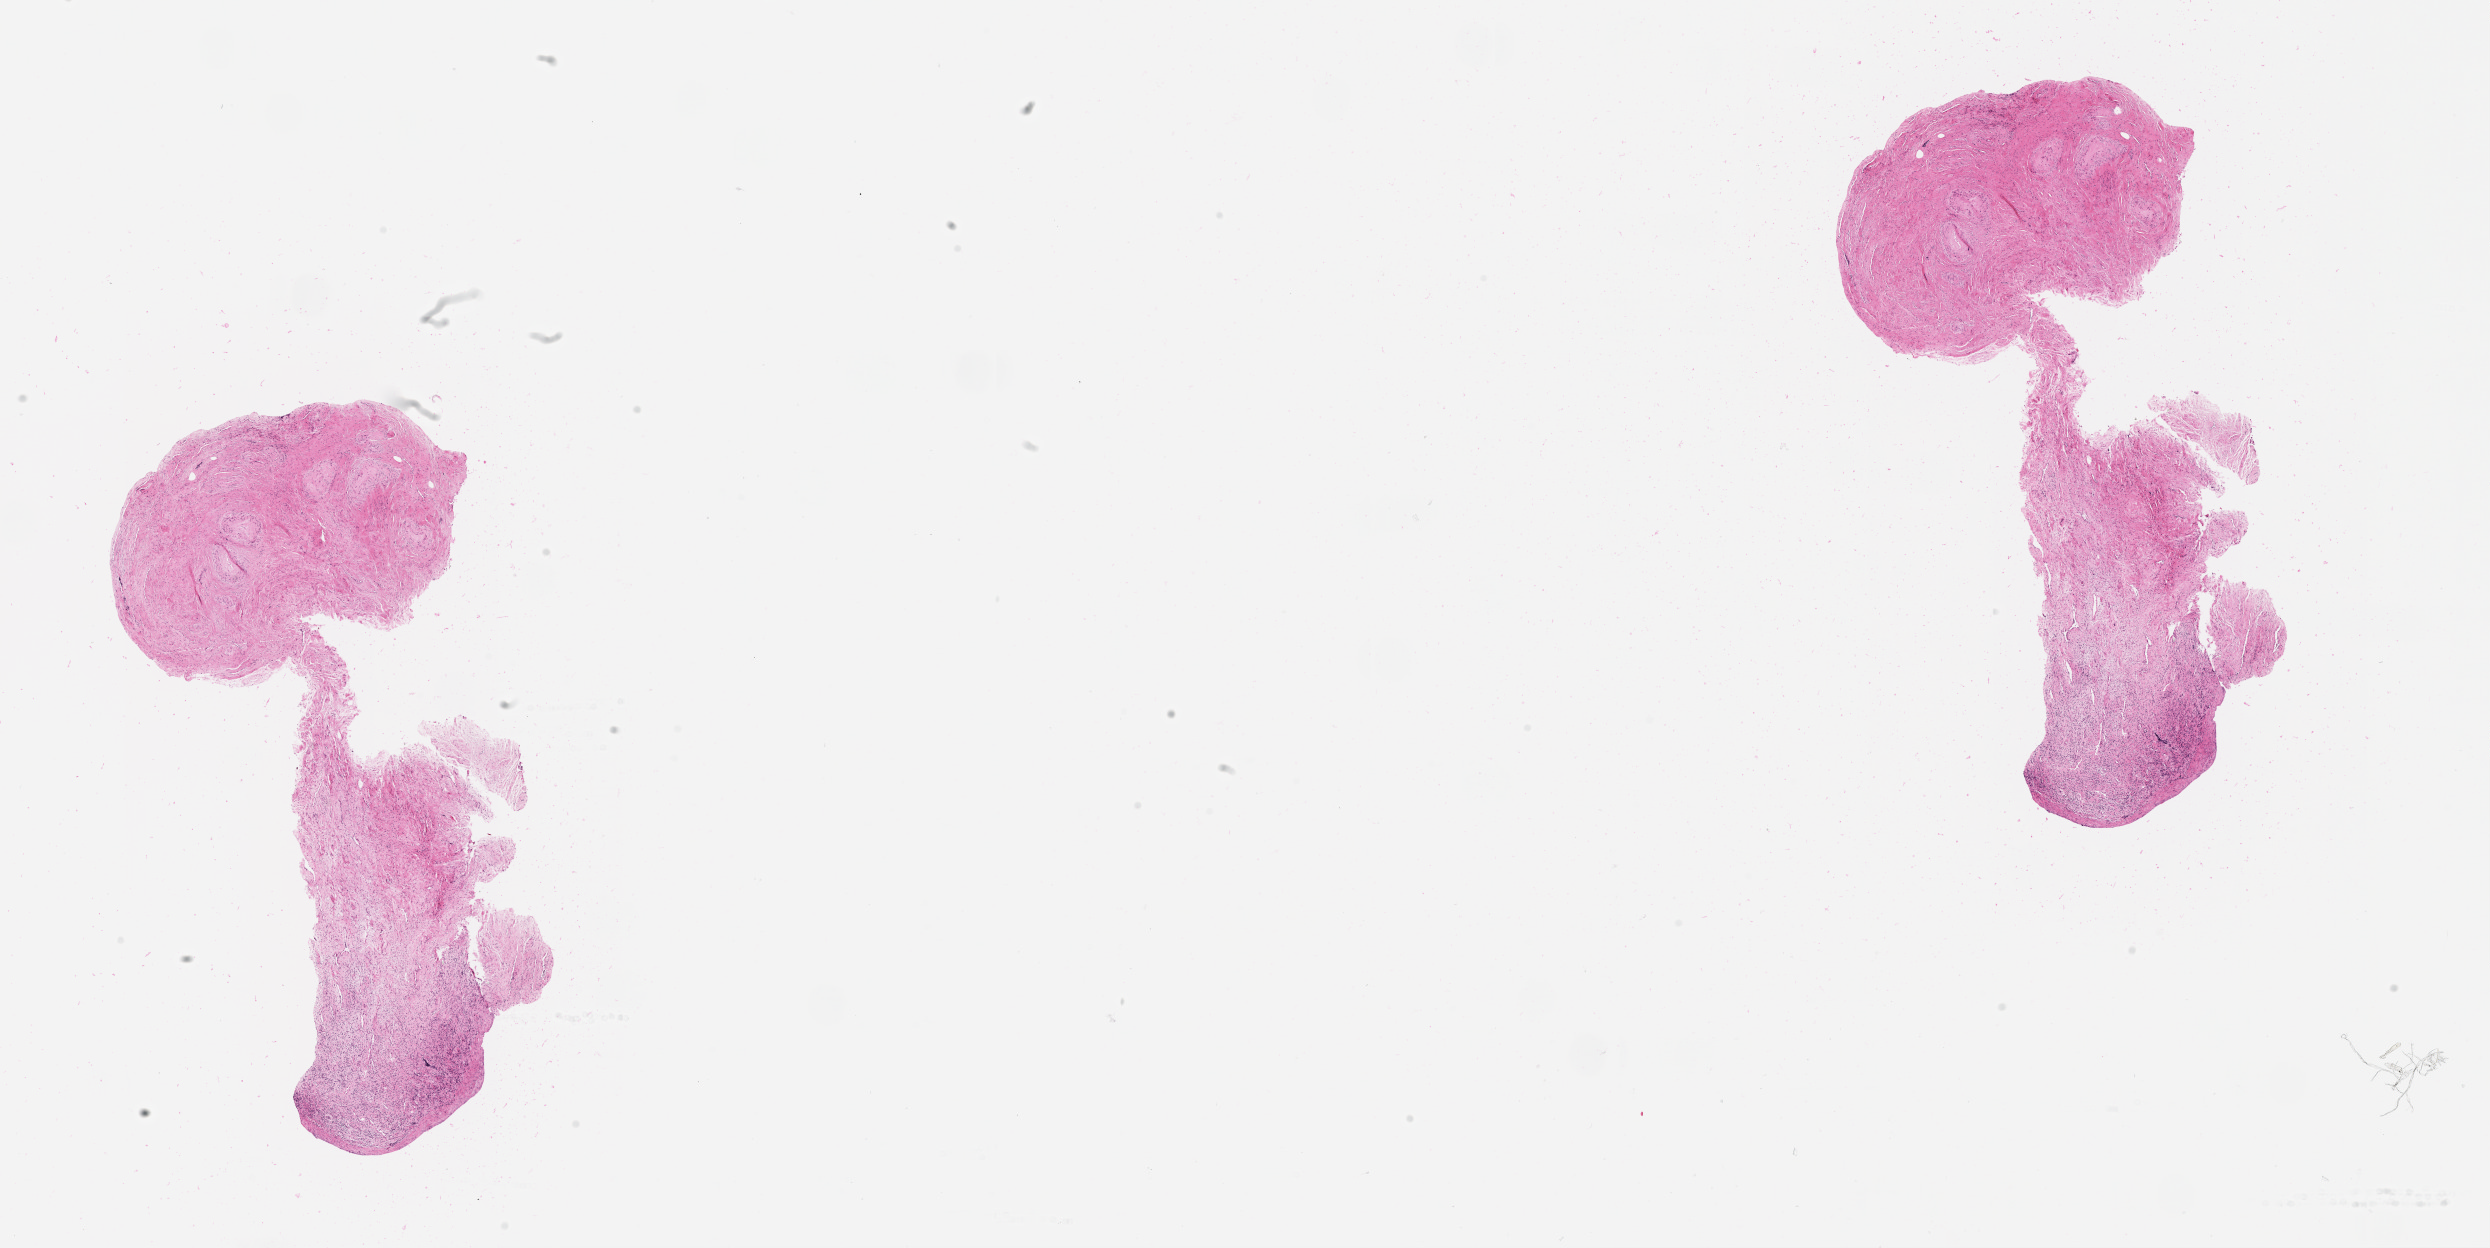
Whole-slide histology image, Hematoxylin and eosin (H&E) stained, whole scanned area (about 20.0 x 10.0 mm) shown as a low-resolution overview; uterus, normal (non-tumour) tissue. Patient: female, age 64 years.
- this section: normal (non-tumour) tissue from the same patient
- patient diagnosis: Endometrioid adenocarcinoma, NOS